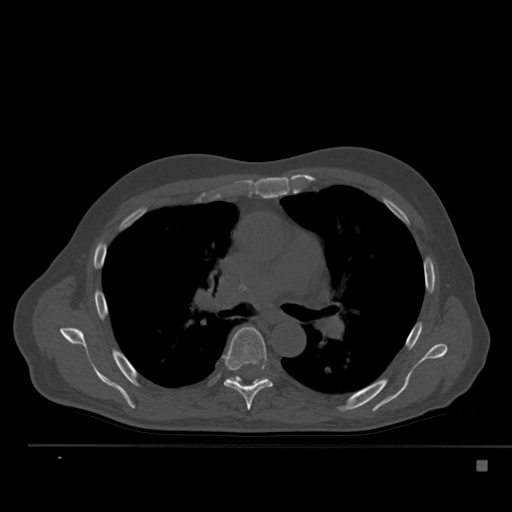
CT including the spine, one axial slice; reconstruction kernel Br40s; 120 kVp; bone window (W 1800 / L 400 HU); 1.5 mm slice thickness; 512 × 512 image matrix, field of view 408 × 408 mm. Male patient, age 70 years. From the clinical record (not read from this slice): primary cancer: renal; vertebrae with lytic lesions (as recorded): T4, T6, T10, T12, L3, L4, L5.
Structures marked on this image (semi-automatic segmentation, software-assisted and operator-edited):
- T6 vertebra: box from (x=222, y=327) to (x=273, y=410) px
- T7 vertebra: (x=228, y=377)–(x=267, y=382)